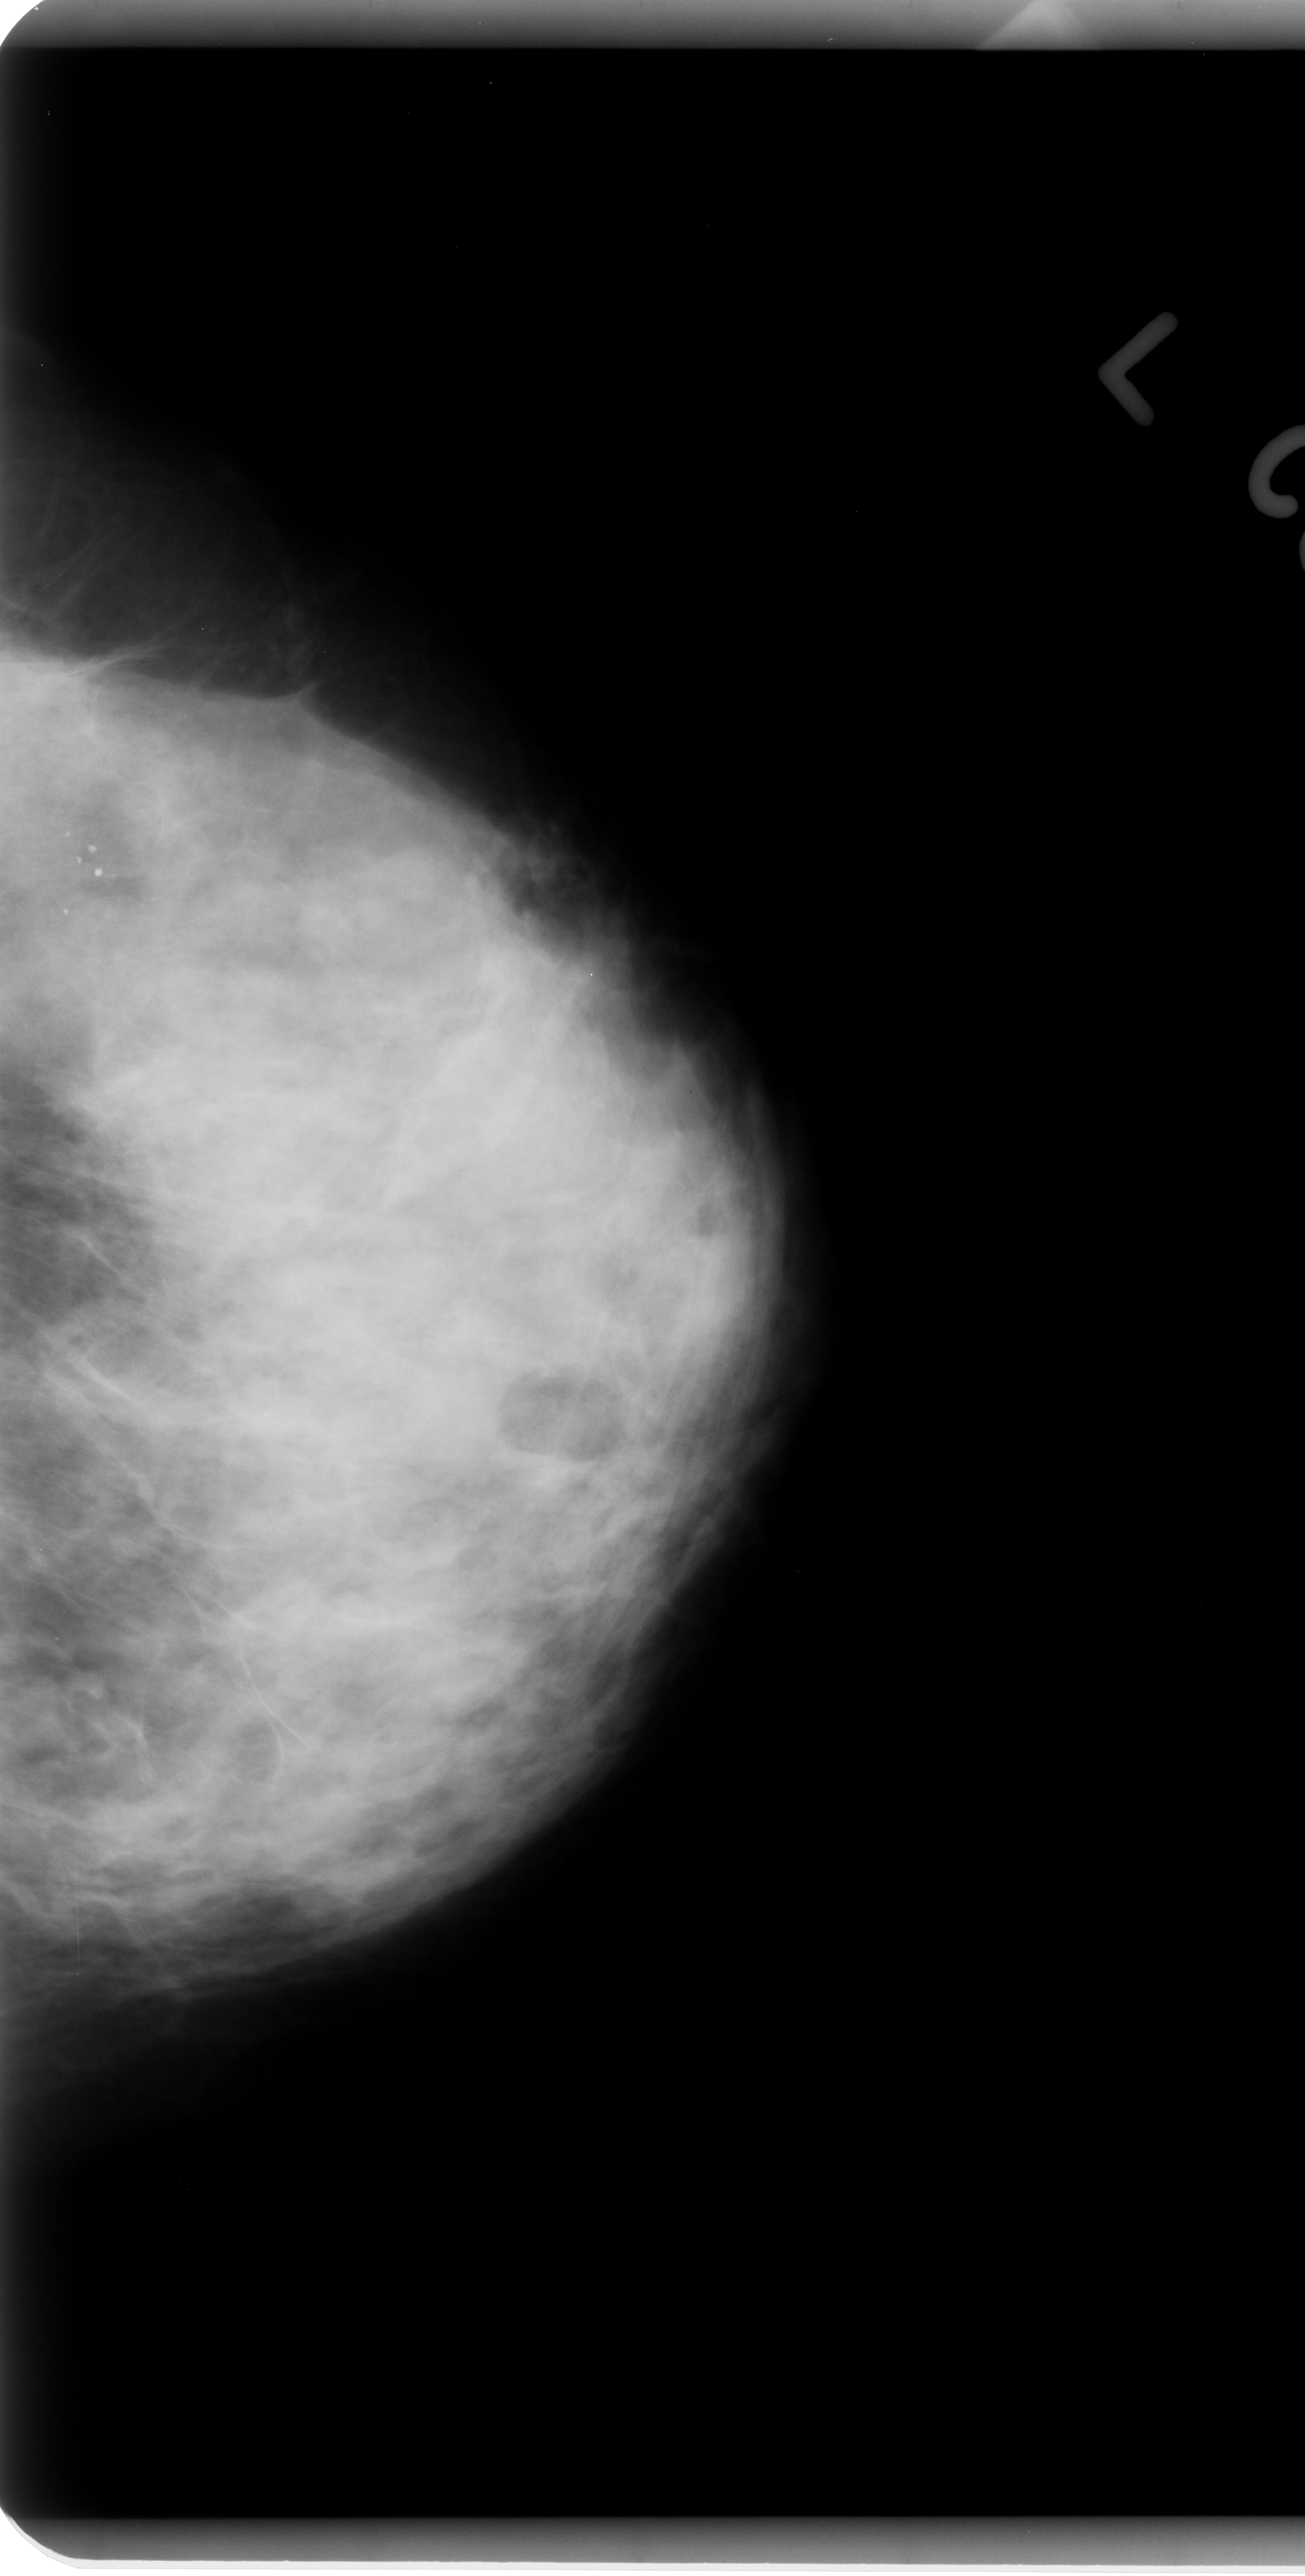
Scanned film-screen mammogram; left breast; craniocaudal (CC) view; BI-RADS breast density category 3 (scale 1–4).
Radiologist-marked abnormalities on this image: calcifications, morphology pleomorphic, distribution clustered; BI-RADS assessment category 4; pathology result (as recorded, not read from the image): benign.